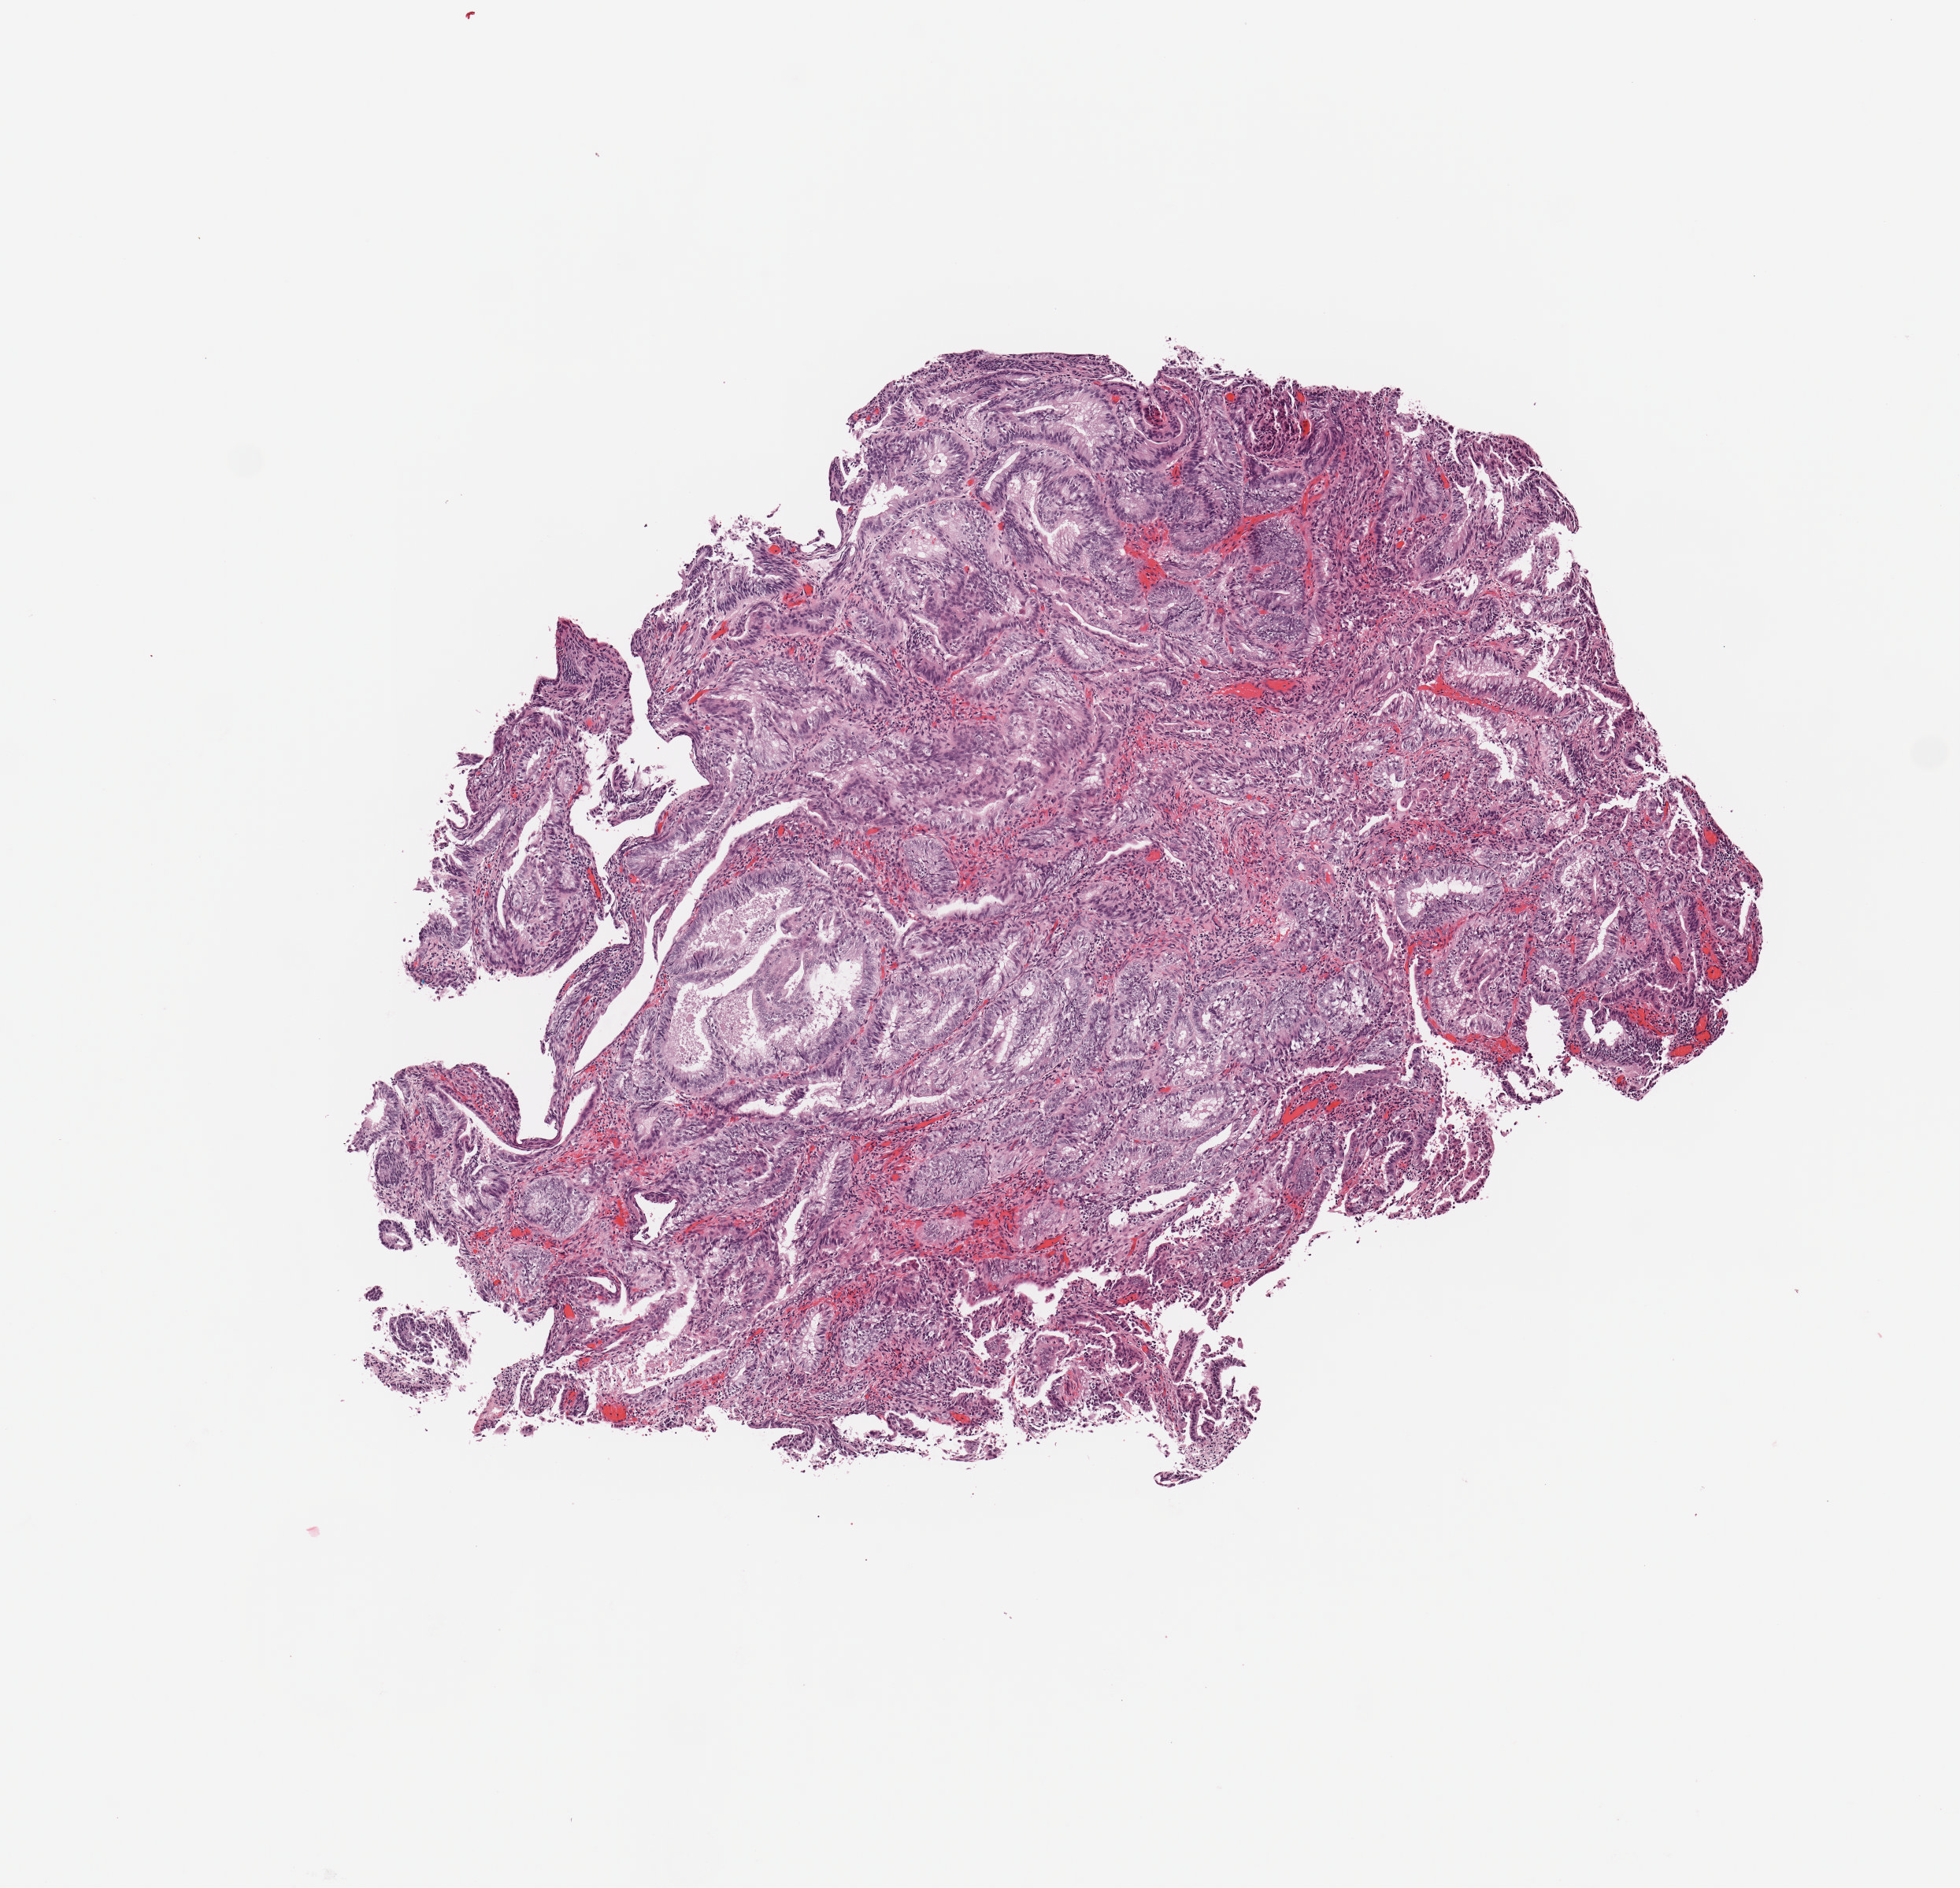
Digitized H&E-stained tissue section (whole slide), a low-resolution overview of the entire scanned area, about 4.9 x 4.7 mm (acquisition: 20x scan). Tumour tissue sample, sampled site: uterus. Patient: female, age 64 years. Histologic grade: G1 (well differentiated). Composition of this section per pathologist review: tumour nuclei 90%, necrosis 2%.
AJCC pathologic stage: I. Diagnosis: Endometrioid adenocarcinoma, NOS.